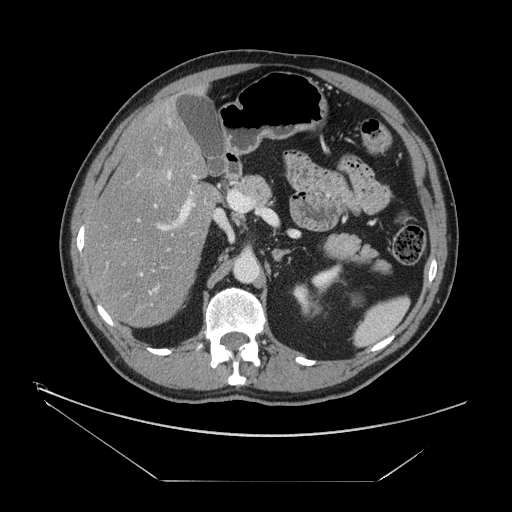
Contrast-enhanced abdominal CT, one axial slice. Position 81 of 161 along the scan axis. Reconstruction kernel STANDARD. 120 kVp. Intravenous contrast given. Soft-tissue window (W 400 / L 40 HU). 2.5 mm slice thickness. 512 × 512 image matrix. Male patient, age 65 years. From the clinical record (not read from this slice): diagnosis: colorectal cancer liver metastases, imaged before liver resection; multiple liver metastases: yes; largest metastasis: 4.2 cm; disease in both lobes: yes.
Structures marked on this image (manually delineated by an expert):
- hepatic veins: bounding box [x1, y1, x2, y2] px = [133, 170, 174, 295]
- liver: [87, 99, 219, 328]
- planned liver remnant (the part of the liver to remain after resection): [103, 100, 212, 327]
- portal vein (with intrahepatic branches): [112, 151, 203, 324]